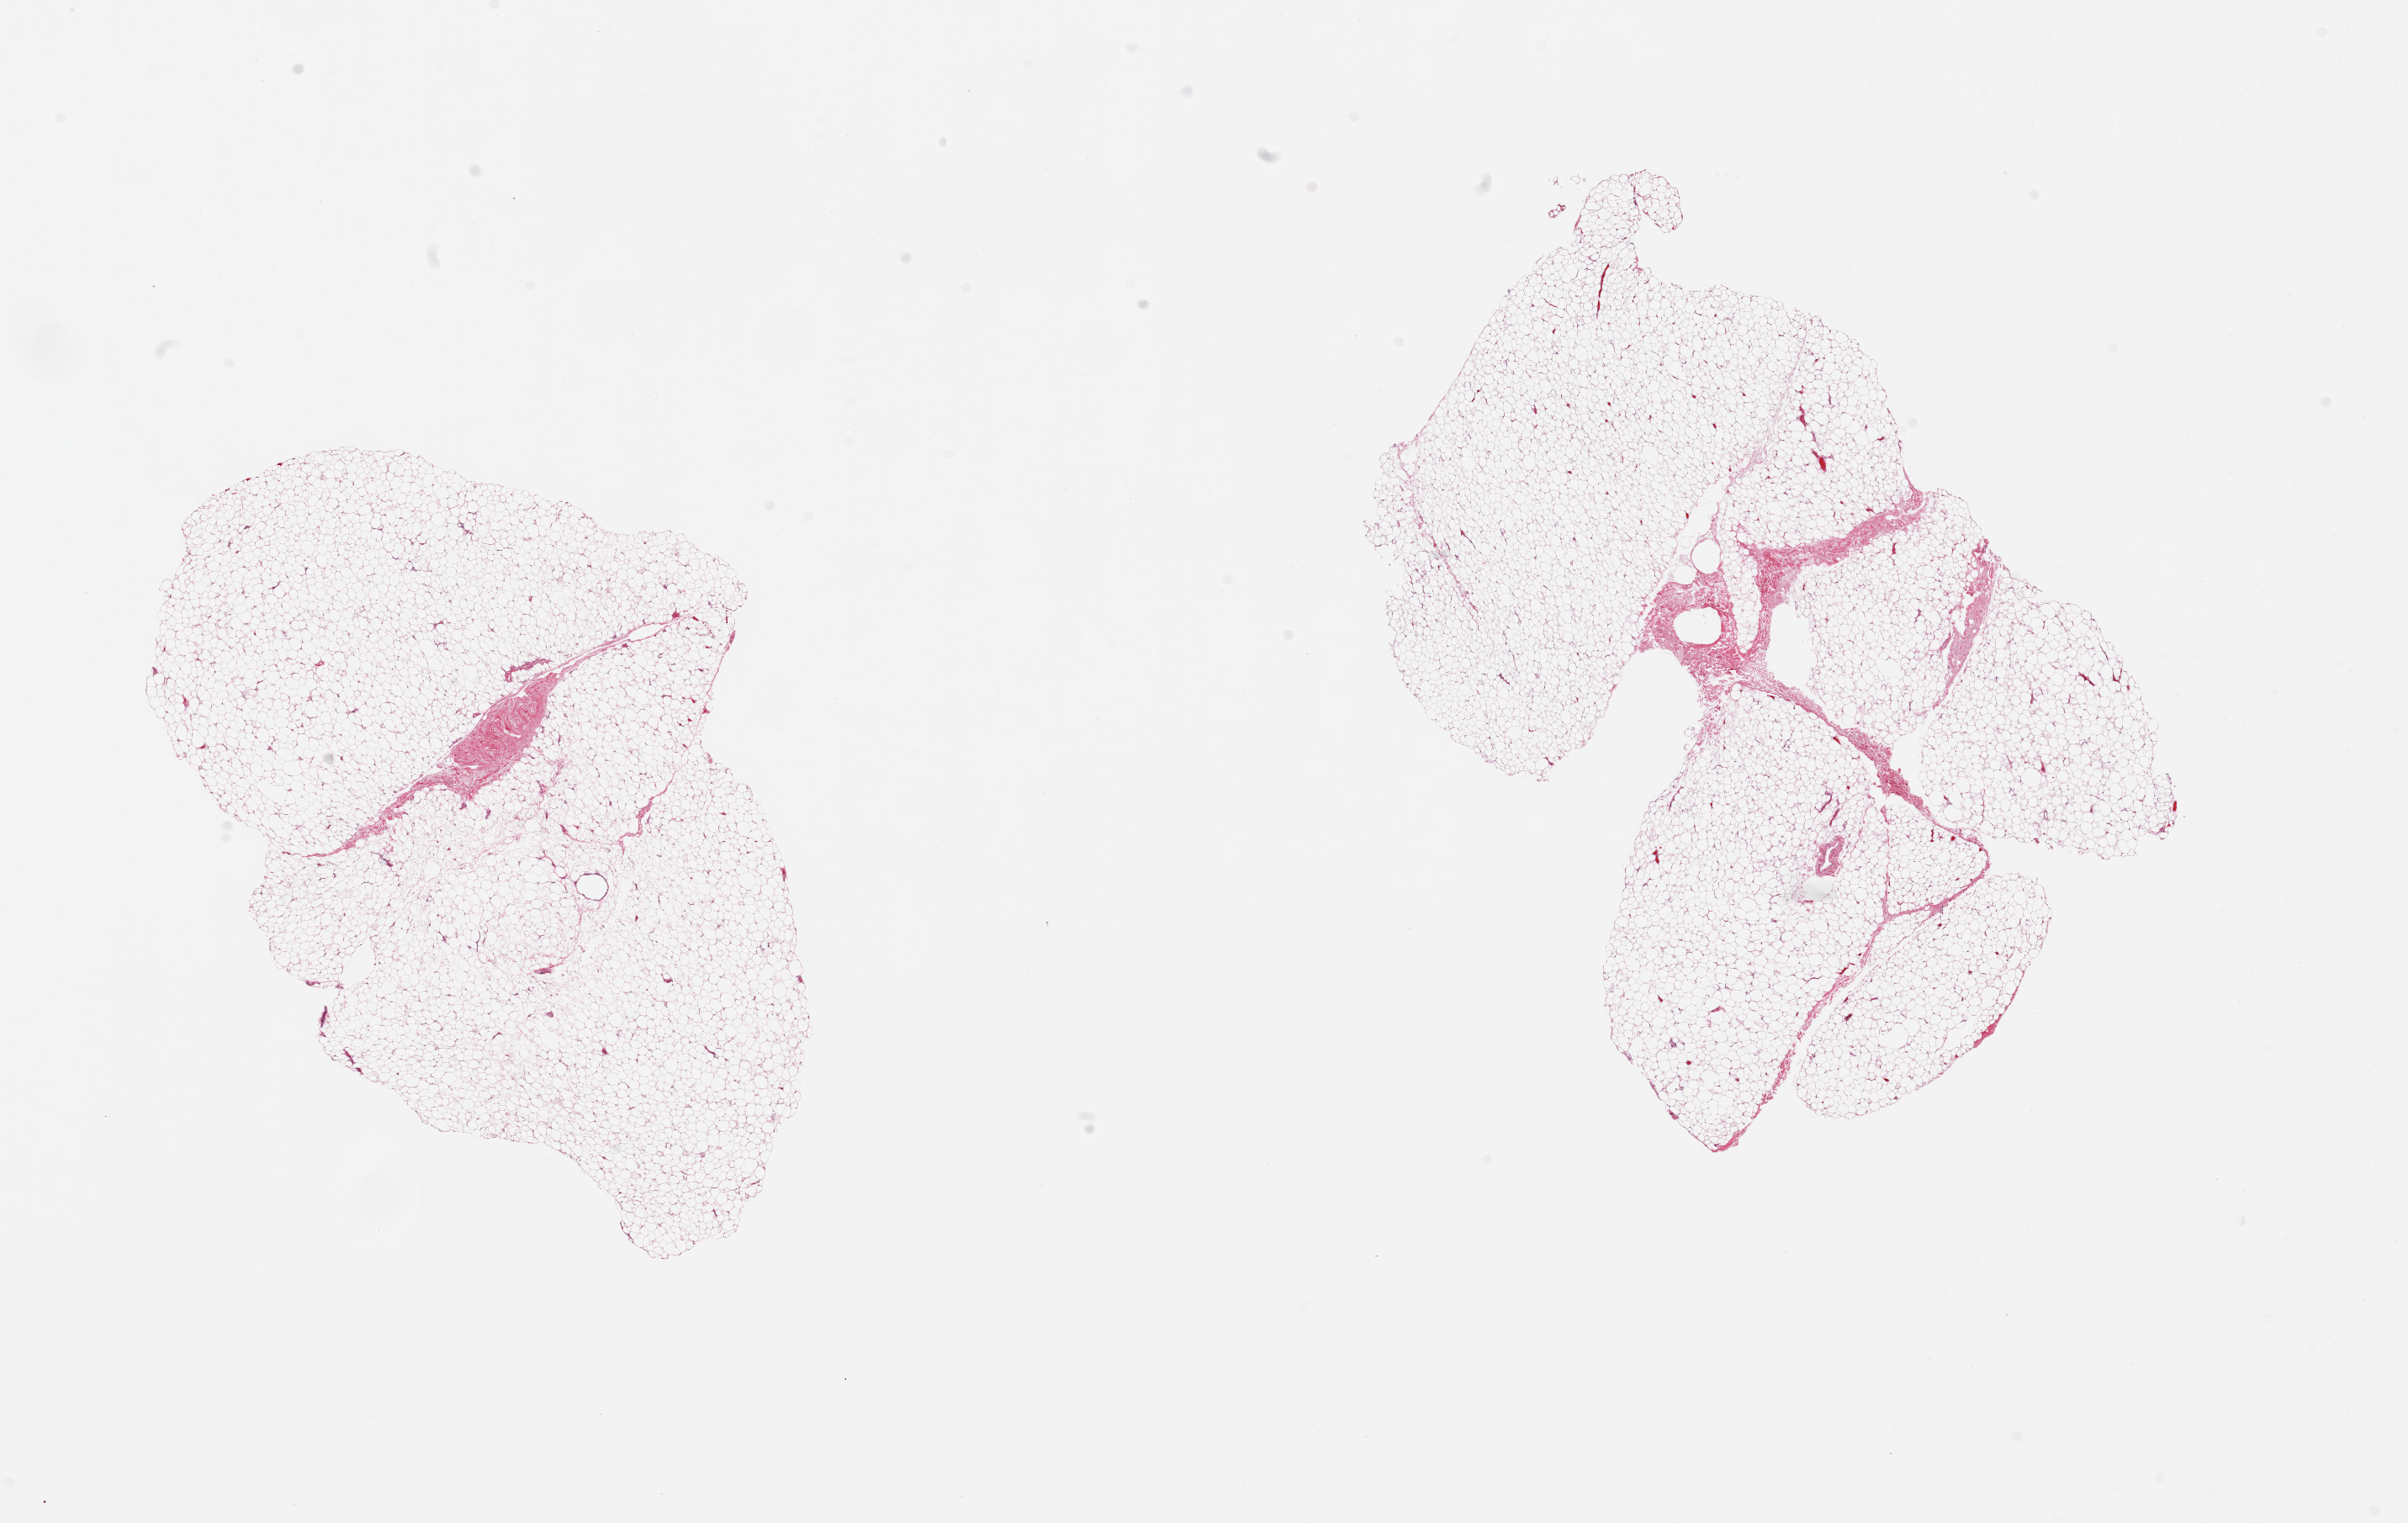
Whole-slide image, H&E stain, brightfield — whole scanned area (about 22.6 x 14.3 mm) shown as a low-resolution overview. PAXgene-fixed, paraffin-embedded tissue. Sampled site (target tissue): breast. Donor tissue sample. Male donor.
Review note (as recorded): 2 pieces; fat with 10% fibrous content; no mammary (ductal) tissue.